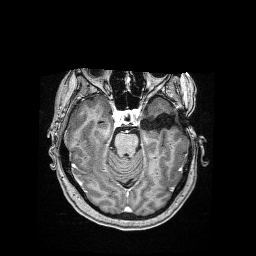
Brain MRI from a brain-tumour surgery series, one axial slice; slice 106 of 176 in the series (ordered by position); T1-weighted post-contrast; 256 × 256 image matrix, field of view 256 × 256 mm. From the clinical record (not read from this slice): histopathology: Dysembryoplastic neuroepithelial tumor; WHO grade: 1; IDH mutation: no; tumour location: Left Temporal.
Annotated regions visible in this slice (outlined manually by an expert reader):
- tumour: box from (x=148, y=113) to (x=151, y=116) px